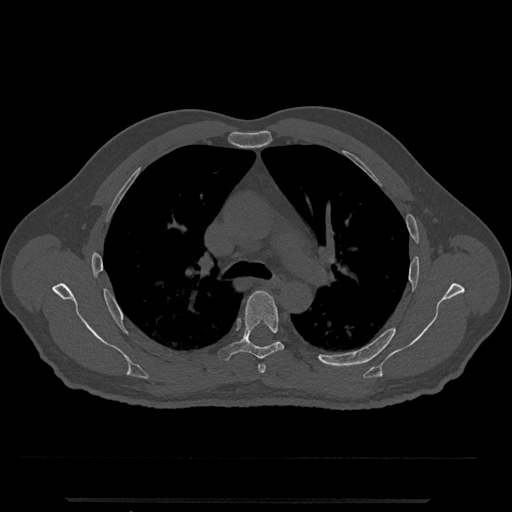
CT including the spine, one axial slice. Position 794 of 797 along the scan axis. Bone window (W 1800 / L 400 HU). 0.5 mm slice thickness. 512 × 512 image matrix, field of view 419 × 419 mm. Male patient, age 63 years. Case-level facts recorded for this patient, not image findings: primary cancer: prostate.
Structures marked on this image (semi-automatically segmented with operator editing):
- T5 vertebra: bounding box <218,290,285,362> (left, top, right, bottom; pixels)
- T6 vertebra: <271,341,278,345>